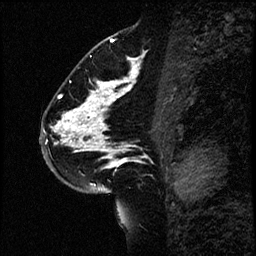
Breast MRI (dynamic contrast-enhanced), one sagittal slice. Position 36 of 60 along the scan axis. Dynamic contrast-enhanced study with each time point stored as its own series, time point 2 of 4 at this slice position (early post-contrast, ordered by acquisition time). 1.5 T. TE 4.2 ms, TR 17.6 ms. 2 mm slice thickness. 256 × 256 image matrix. Female patient, age 43 years. Case-level facts recorded for this patient, not image findings: setting: breast cancer imaged before/during neoadjuvant chemotherapy.
Outlined on this slice (semi-automatically segmented with operator editing):
- analysis volume of interest (the breast-tissue region the enhancement analysis was run in; not a lesion): bounding box (x1, y1, x2, y2) in pixels: (42, 57, 168, 191)
- tumour enhancement mask (voxels above the 100 % enhancement threshold inside the analysis volume of interest): (46, 57, 140, 185)